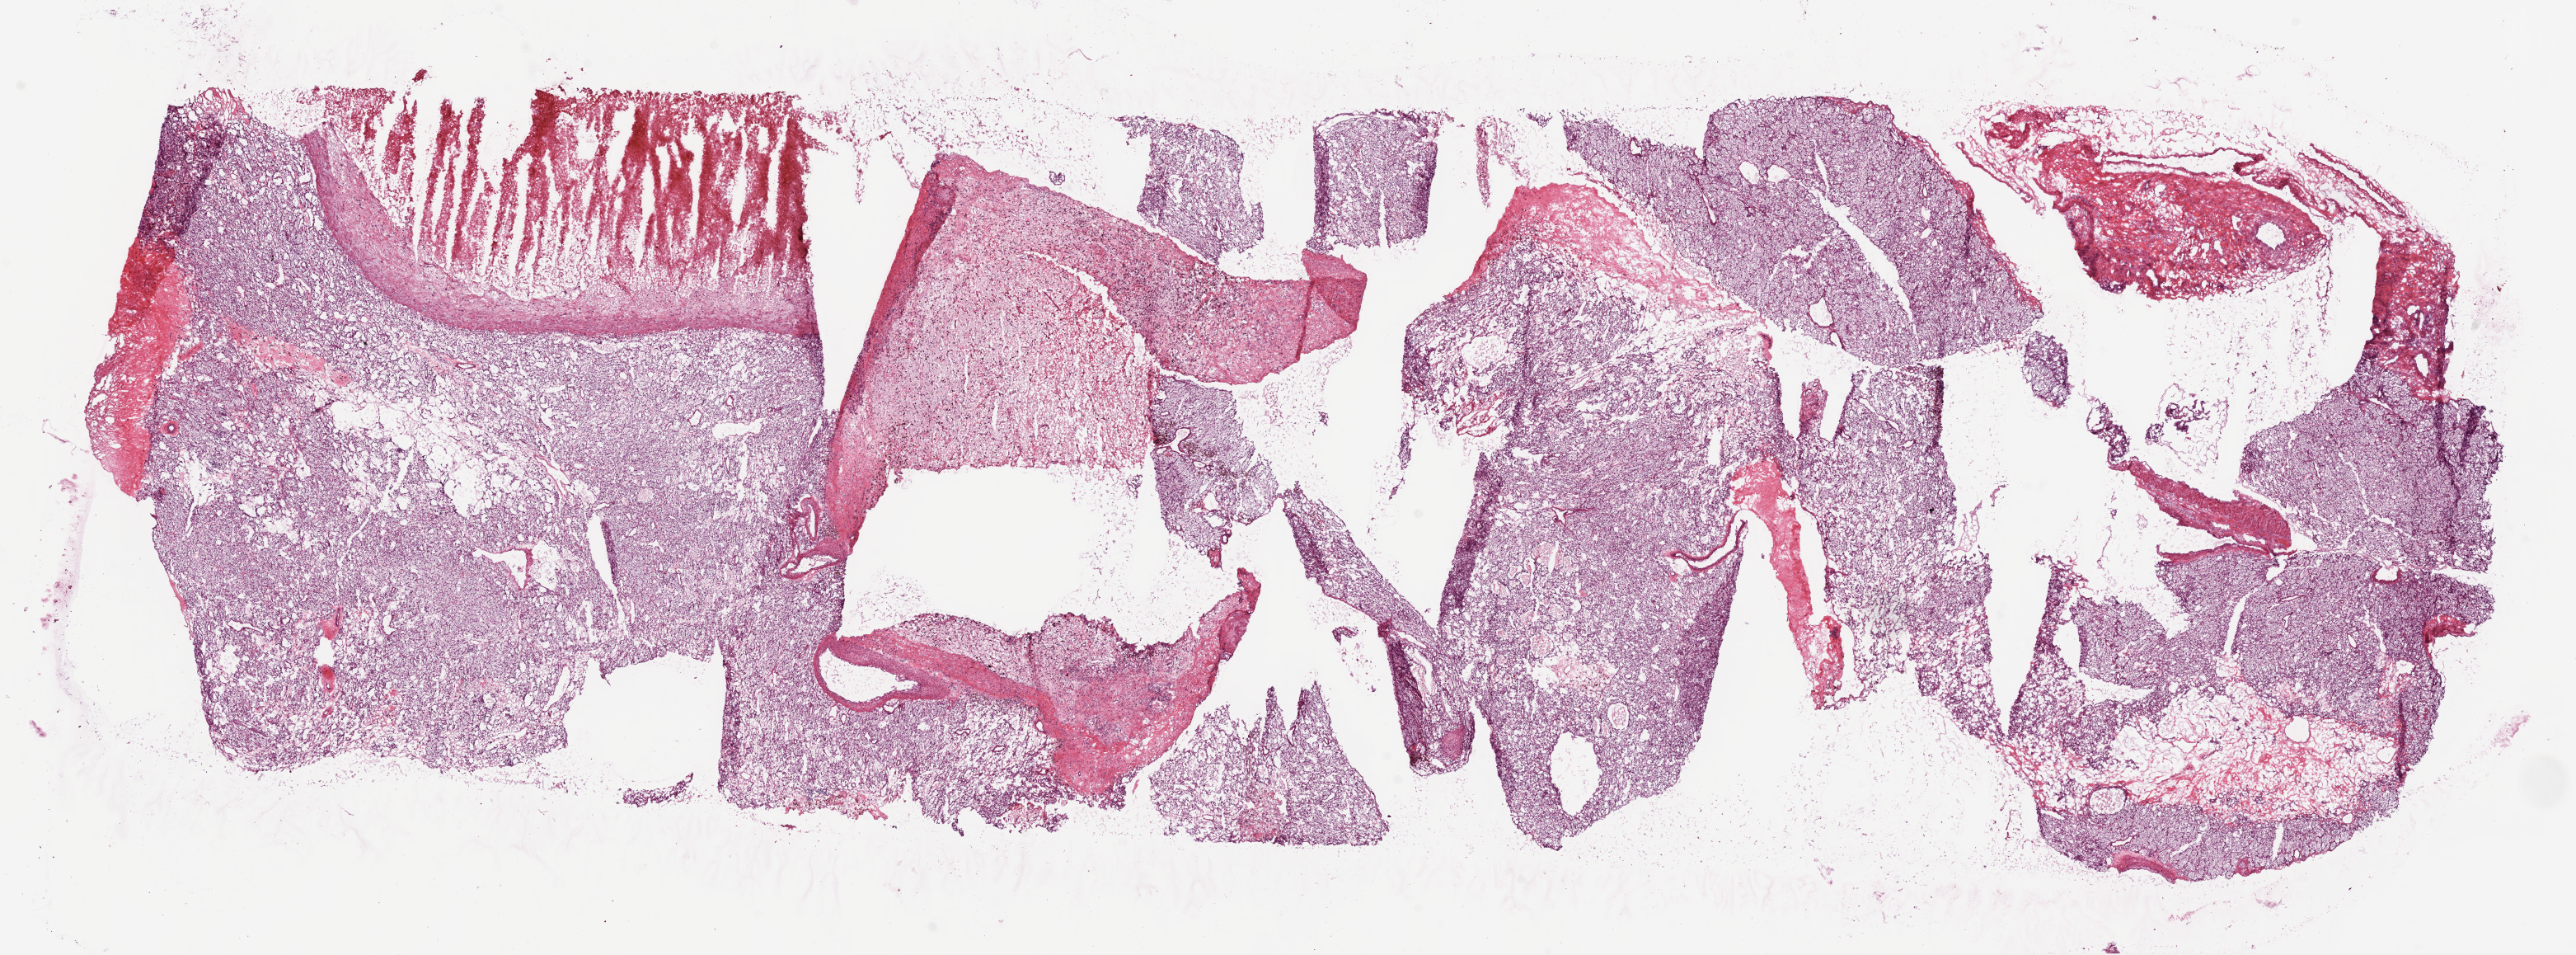
H&E-stained whole-slide image — a low-resolution overview of the entire scanned area, about 25.1 x 9.3 mm; frozen section from the bottom of the tissue portion; kidney, primary tumour sample. Male patient; age at initial diagnosis 42 years. Histologic grade: G2 (moderately differentiated). Composition of this section per pathologist review: tumour cells 60%, tumour nuclei 80%, normal cells 0%, stromal cells 40%, necrosis 0%.
Pathologic diagnosis: Clear cell adenocarcinoma, NOS. AJCC pathologic stage: I.